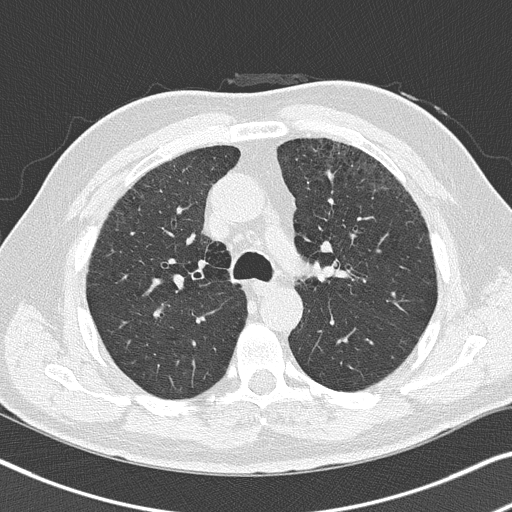
Axial slice from a low-dose chest CT screening exam. Baseline screening round. Lung window (W 1500 / L -600 HU). 2 mm slice thickness. Male participant, aged 64 years at enrolment.
Expert-annotated lung lesion, bounding box [x1, y1, x2, y2] px = [321, 250, 354, 279]. The exam's reader record, not a measurement of the box and not confirmed to be the same lesion: non-calcified nodule or mass ≥4 mm, left upper lobe, 4 × 4 mm, smooth margins, soft tissue attenuation. Participant outcome: lung cancer diagnosed 450 days after this screen (after the second annual screen) — squamous cell carcinoma, keratinizing, NOS, left upper lobe, moderately differentiated (G2), stage IA (AJCC 6th edition), 4 mm at pathology.